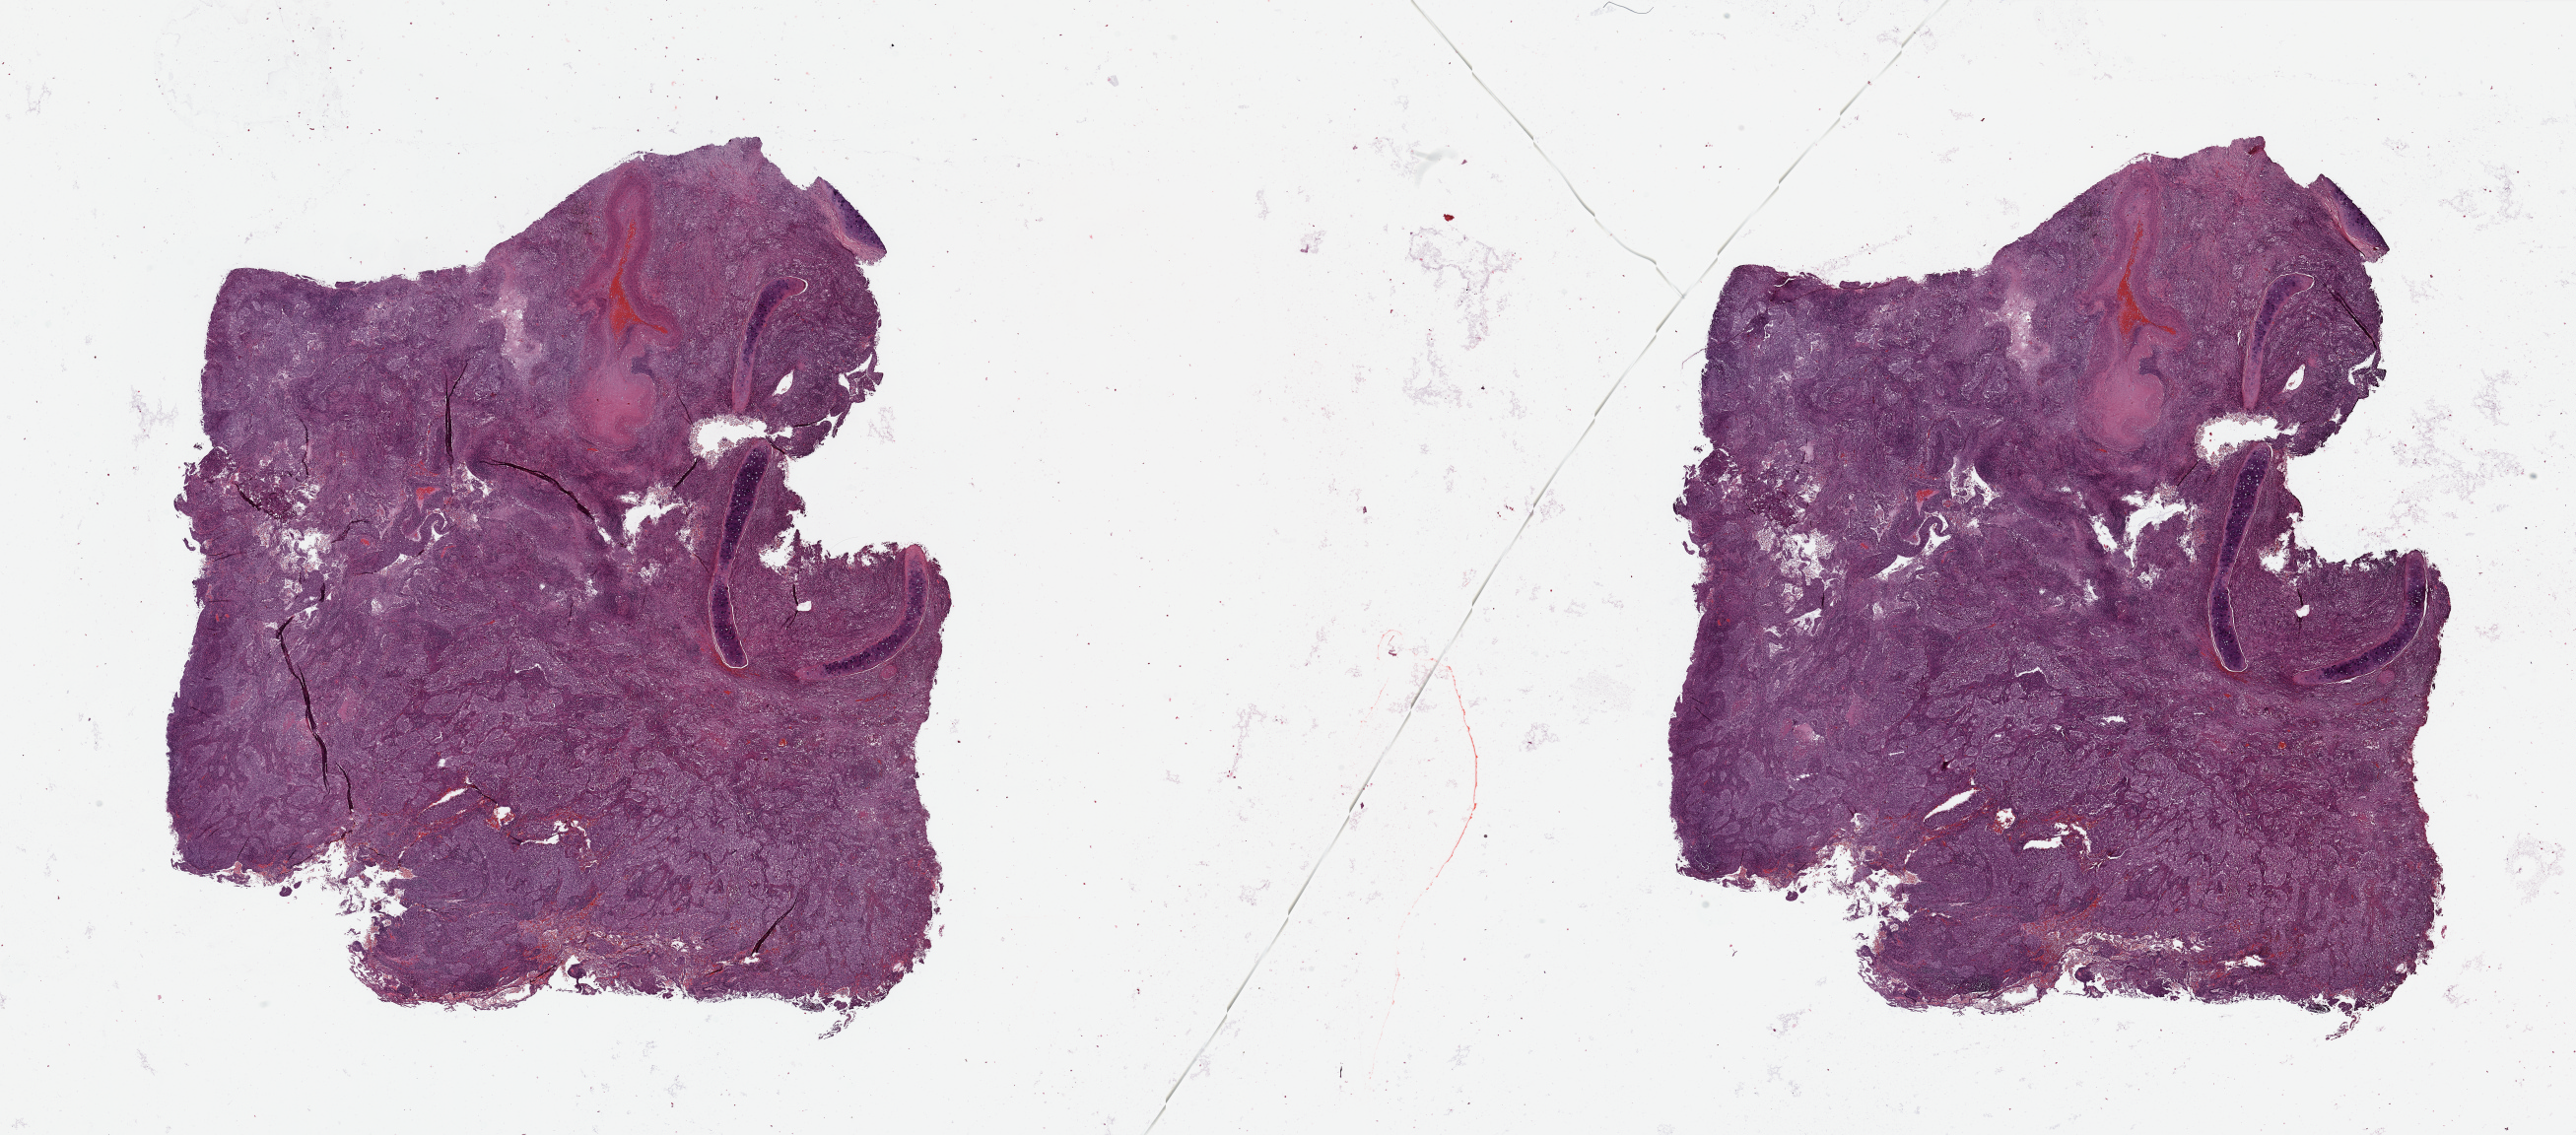
Digitized H&E tissue section (whole slide), a low-resolution overview of the entire scanned area, about 41.3 x 18.2 mm; tumour tissue sample, lung. Patient: male, age 72 years. Histologic grade: G3 (poorly differentiated).
* diagnosis: Adenocarcinoma, NOS
* AJCC pathologic stage: IB
* primary tumour site (as recorded): left upper lobe